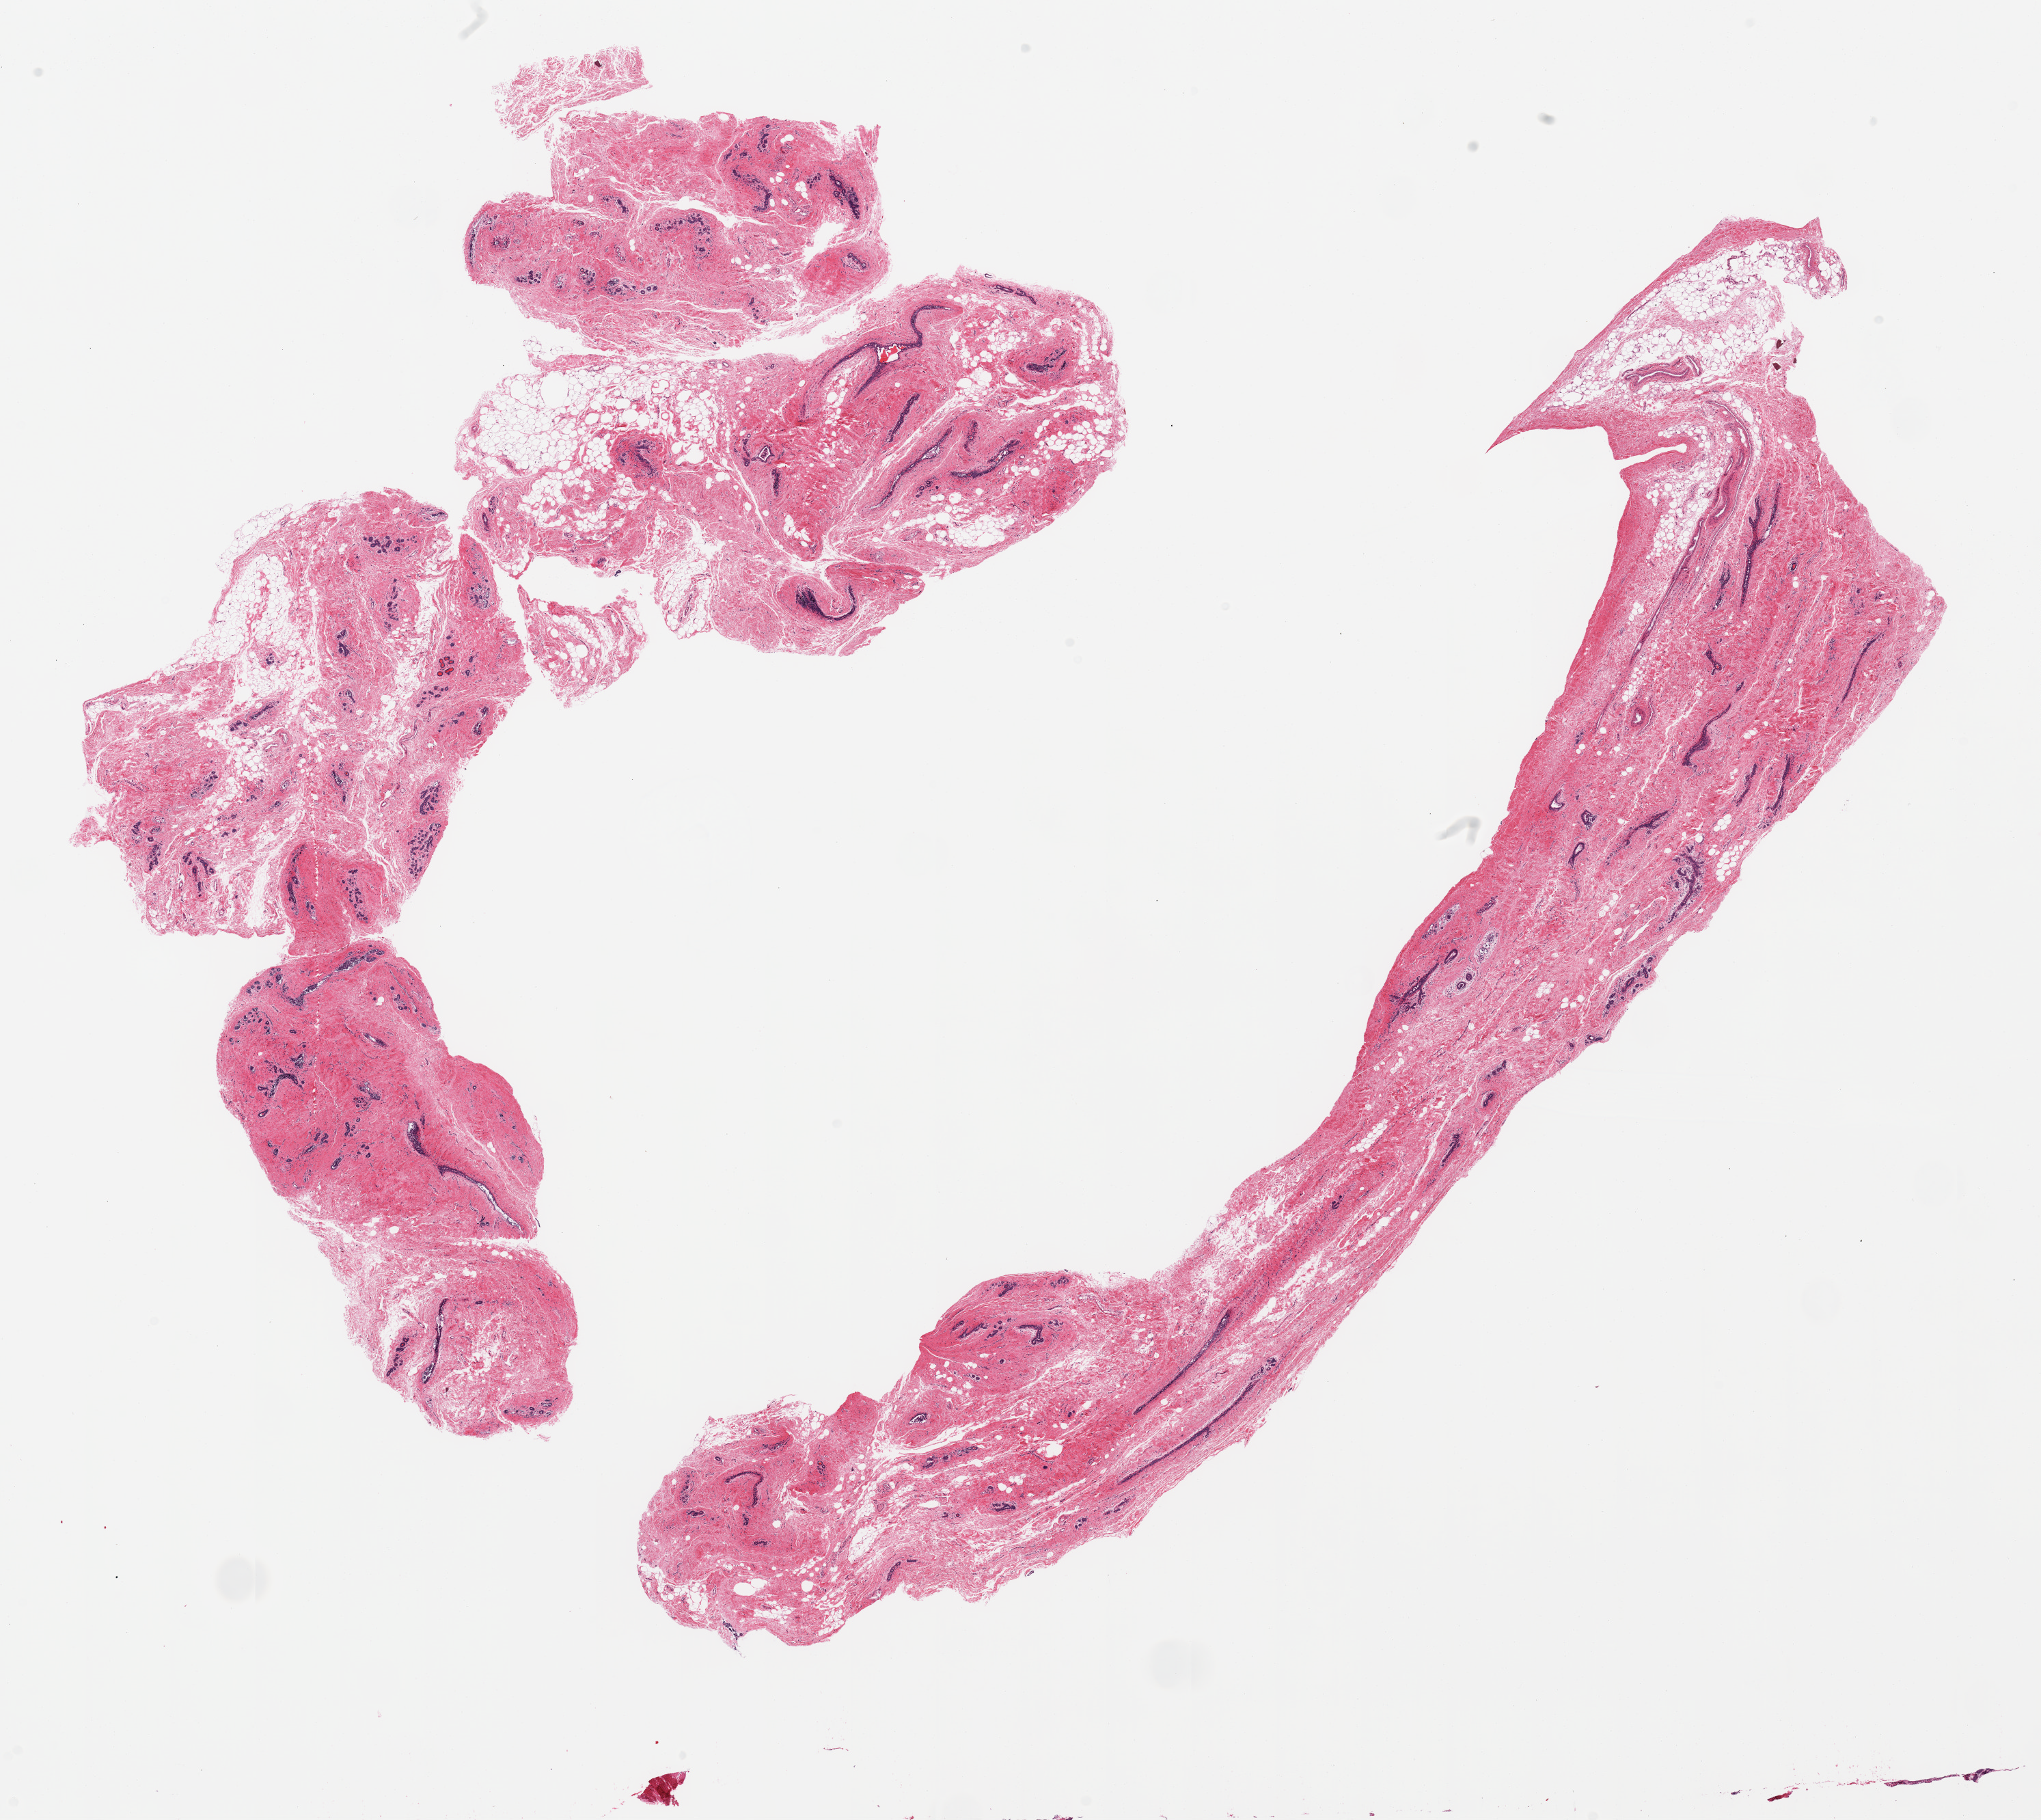
Haematoxylin and eosin whole-slide image — whole scanned area (about 23.6 x 21.1 mm, from a 20x scan) shown as a low-resolution overview, PAXgene-fixed paraffin-embedded (PFPE) section, section of breast (target tissue), tissue donor sample. Female donor.
Reviewer comment on this tissue sample: 2 pieces, predominantly fibrous stroma with ducts/lobules, ~20% fat.